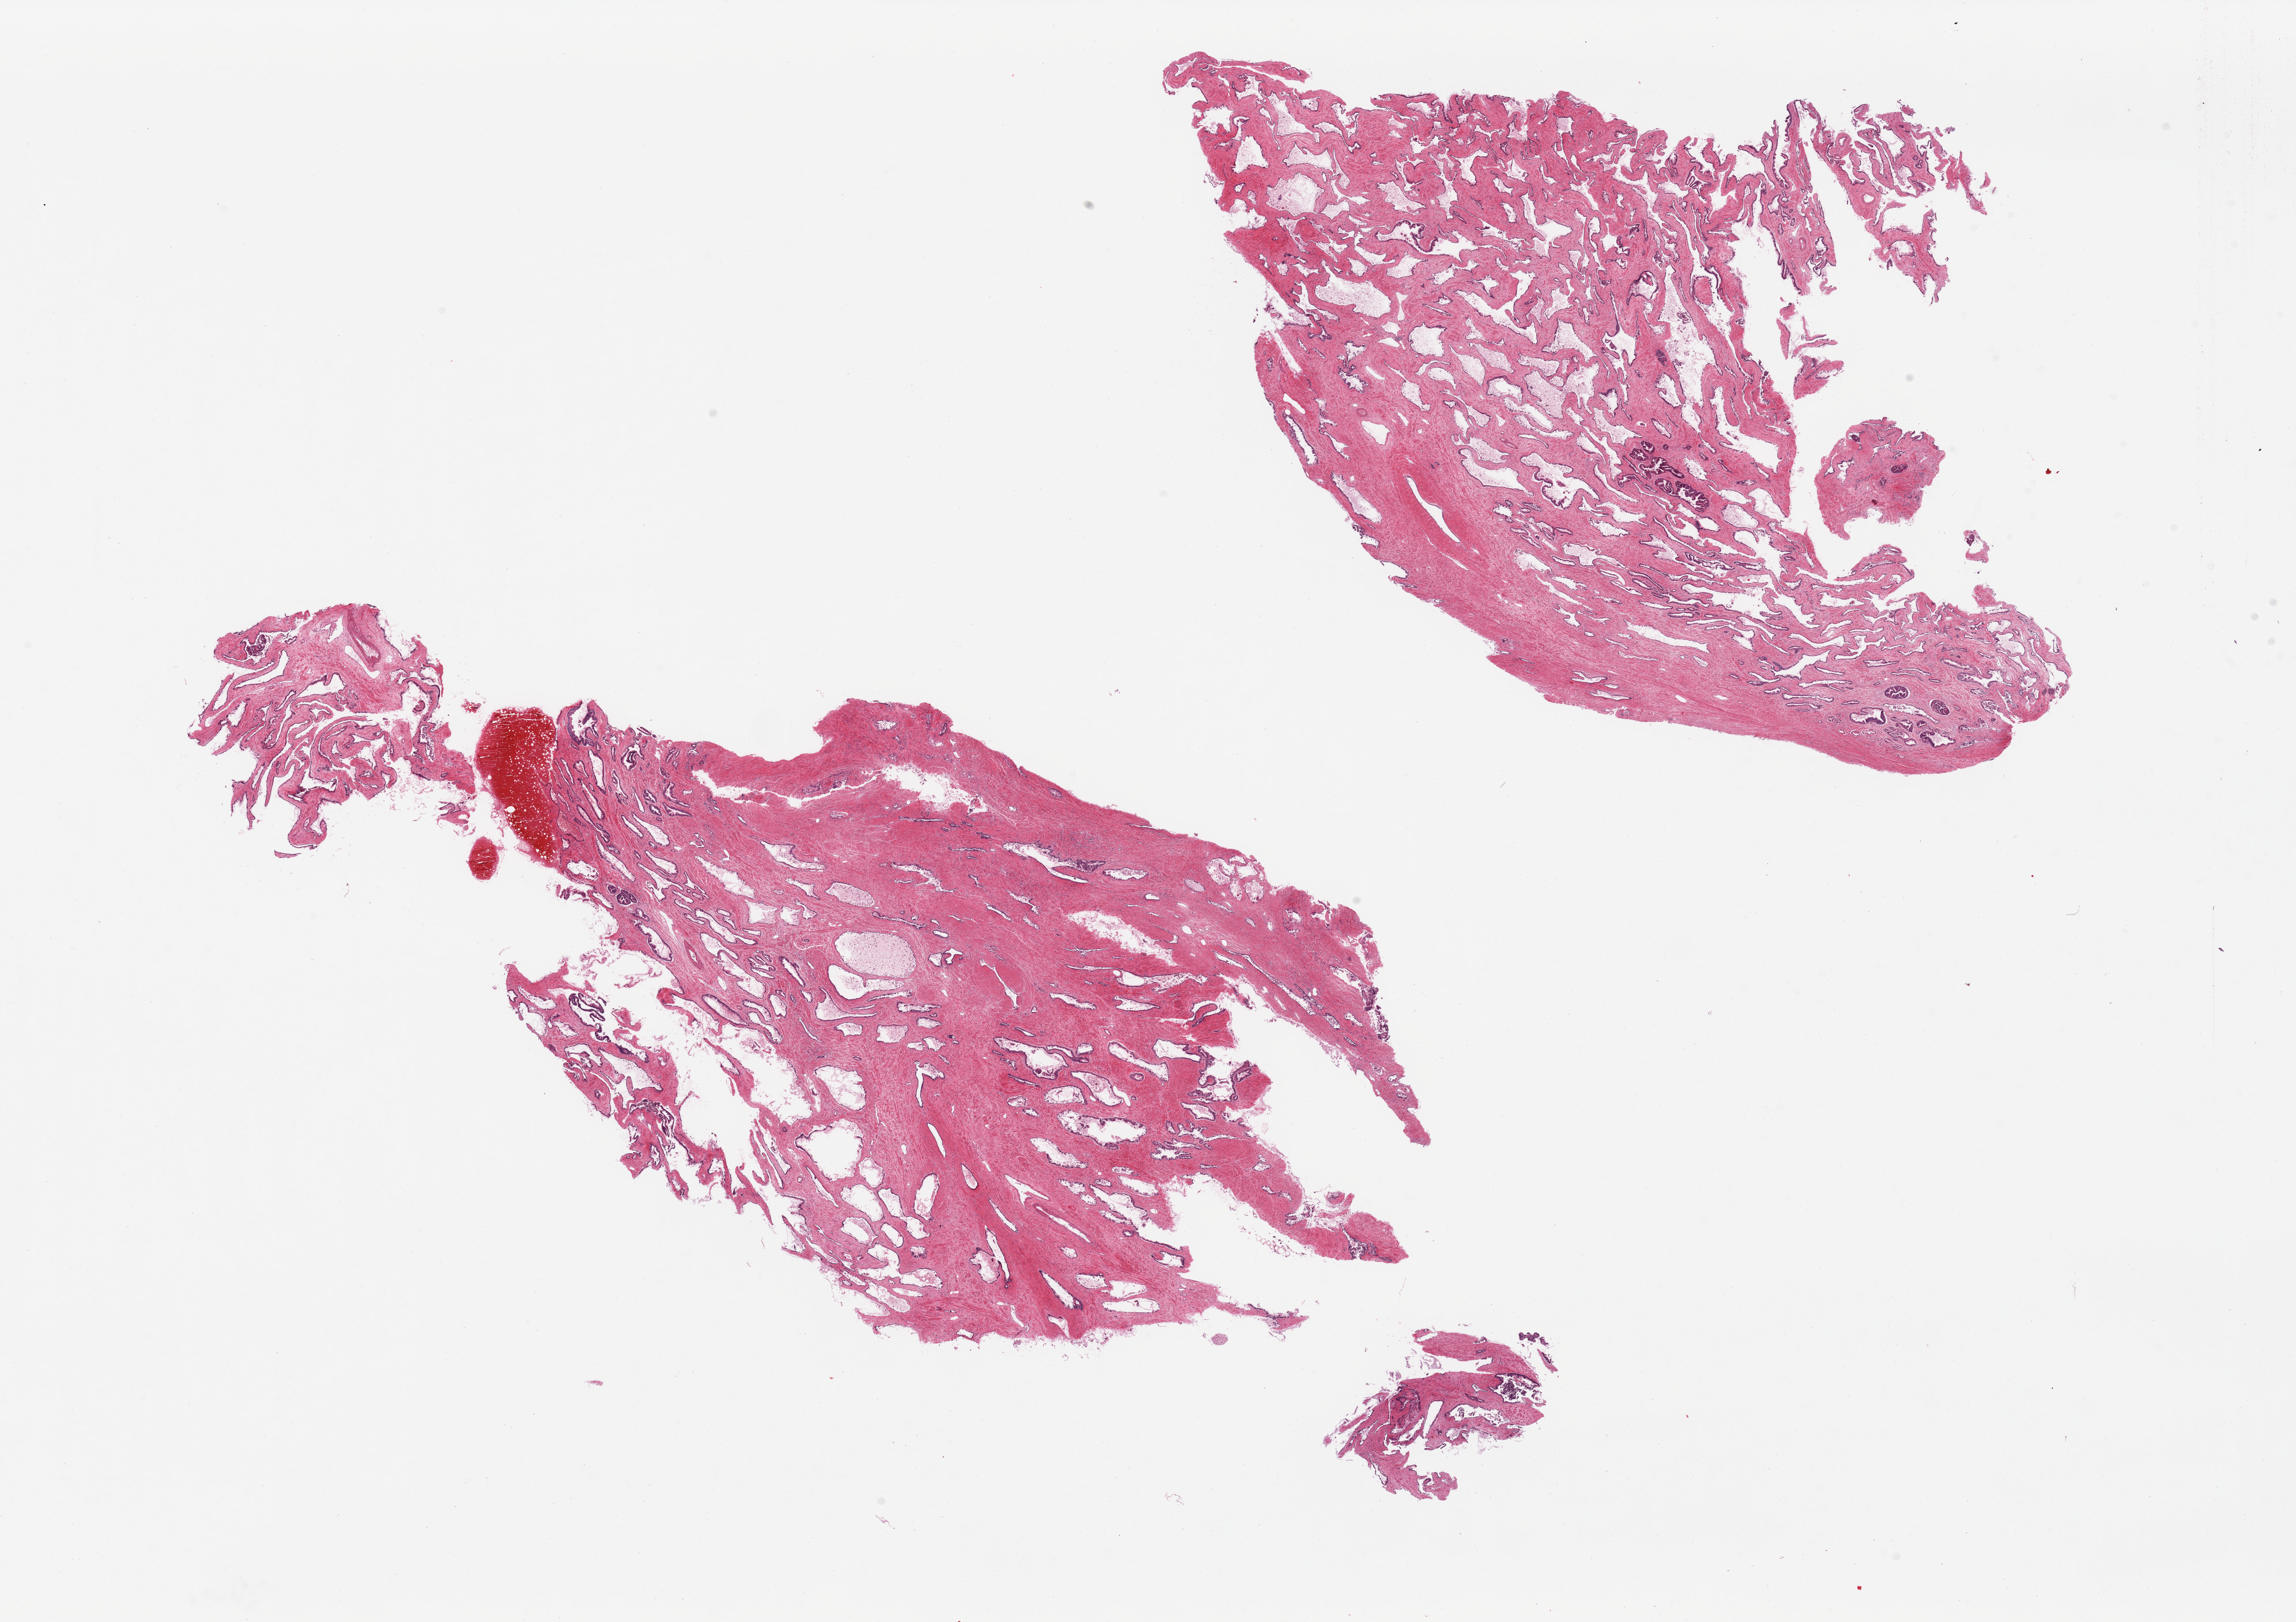
Hematoxylin and eosin (H&E) whole-slide image — shown as a low-resolution overview of the whole scanned area (about 31.5 x 22.2 mm), PAXgene-fixed paraffin-embedded (PFPE) section, section of prostate (target tissue), tissue donor sample. Donor: male.
Review note (as recorded): 2 pieces, epithelium sloughing.